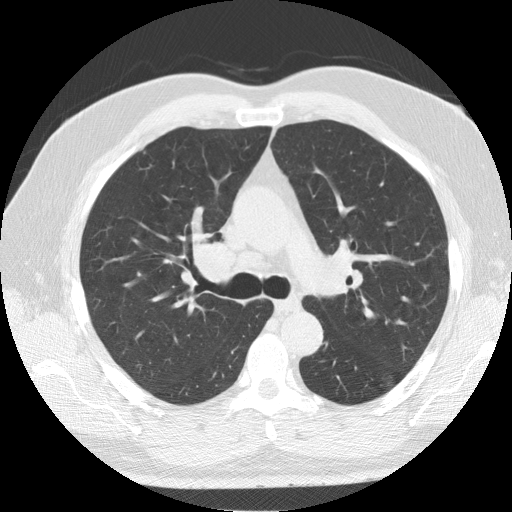
Low-dose screening chest CT, one axial slice; slice 93 of 139 in the series (ordered by position); reconstruction kernel STANDARD; 120 kVp; lung window (W 1500 / L -600 HU); 512 × 512 image matrix, field of view 376 × 376 mm.
Outlined on this slice (outlined manually by an expert reader):
- lesion 1 (tumor, upper lobe of right lung): box from (x=196, y=240) to (x=235, y=282) px